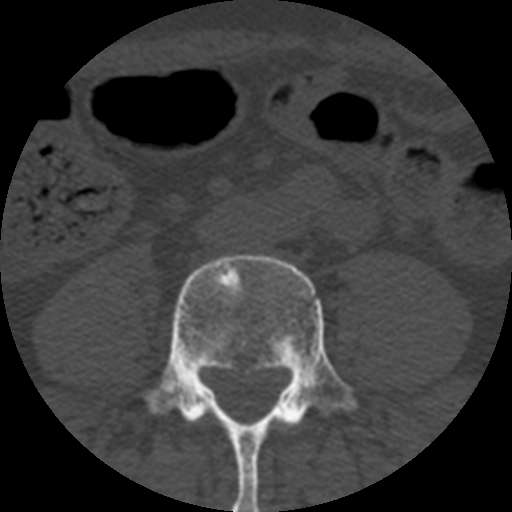
CT including the spine, one axial slice. Slice 92 of 508 in the series (ordered by position). Reconstruction kernel STANDARD. 120 kVp. Bone window (W 1800 / L 400 HU). 1.25 mm slice thickness. 512 × 512 image matrix, field of view 160 × 160 mm. Patient age 57 years. Case-level facts recorded for this patient, not image findings: primary cancer: prostate.
Structures marked on this image (semi-automatically segmented with operator editing):
- L4 vertebra: bounding box <138,254,358,512> (left, top, right, bottom; pixels)